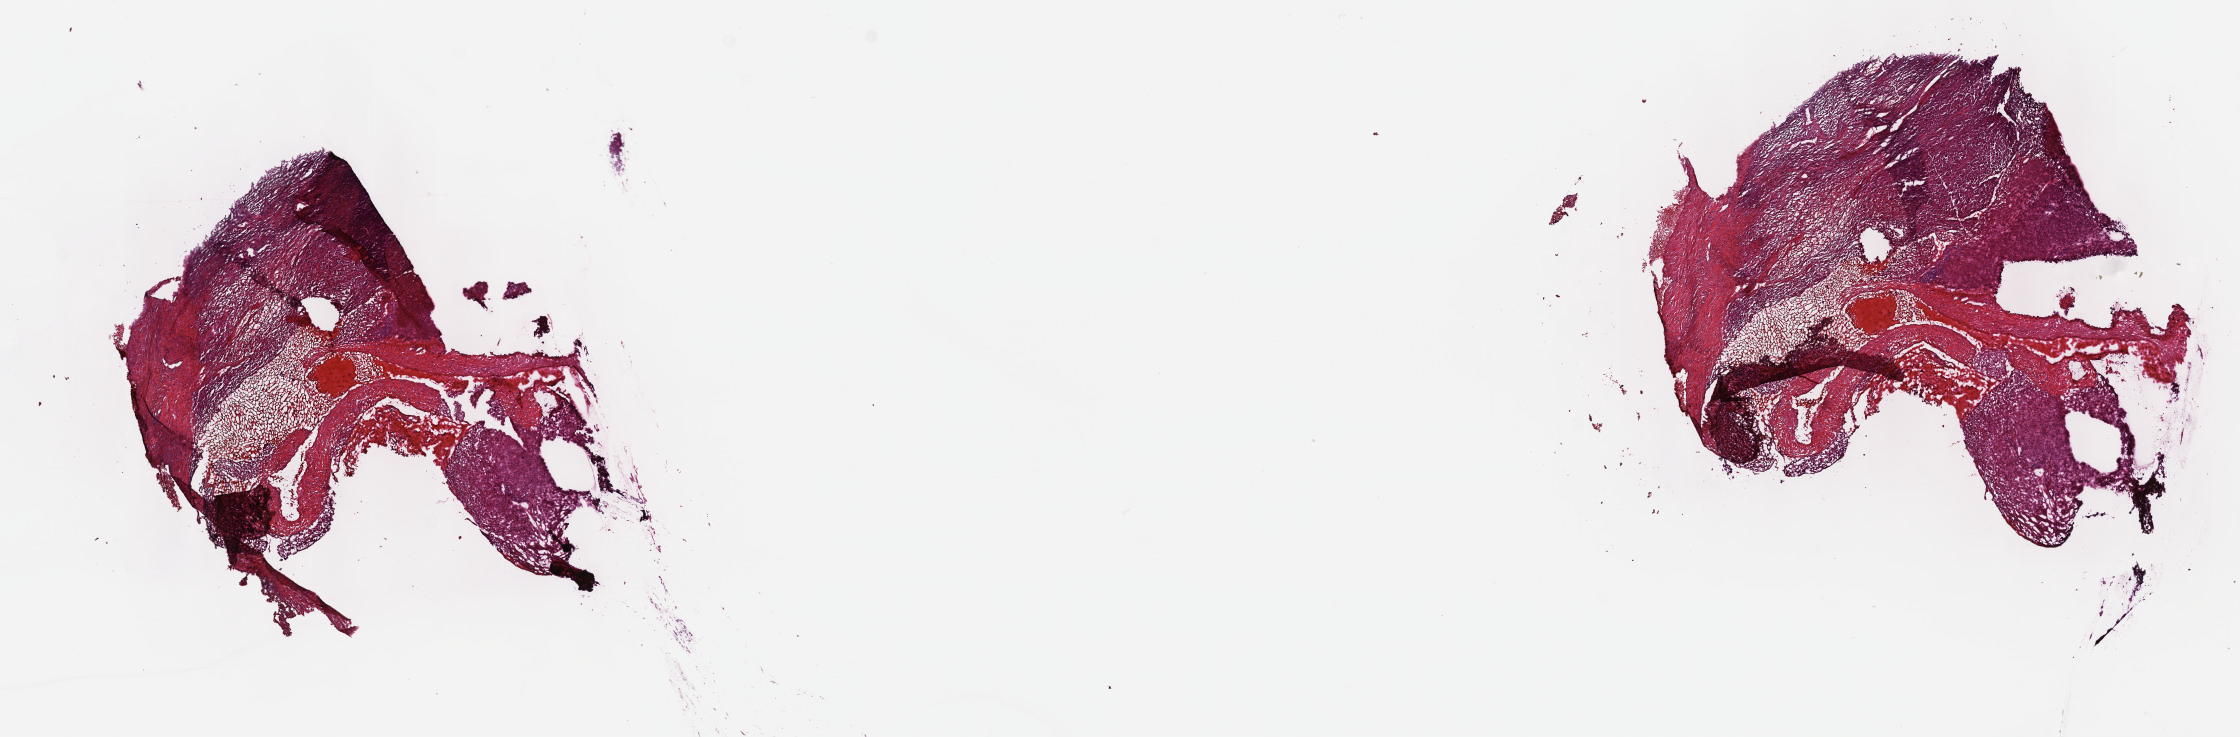
Whole-slide histology image, Hematoxylin and eosin (H&E) stained — low-resolution overview of the scanned area, about 18.1 x 6.0 mm; frozen section; liver, primary tumour sample. Male patient; age at initial diagnosis 29 years. Histologic grade: G2 (moderately differentiated). Pathologist review of this section (percent, as recorded): tumour cells 30%, tumour nuclei 75%, normal cells 0%, stromal cells 60%, necrosis 10%. Infiltration values recorded for this section: lymphocyte infiltration 4%, monocyte infiltration 1%, neutrophil infiltration 1%.
* AJCC pathologic stage: IIIA
* histologic diagnosis: Hepatocellular carcinoma, NOS
* TNM: T3a N0 M0